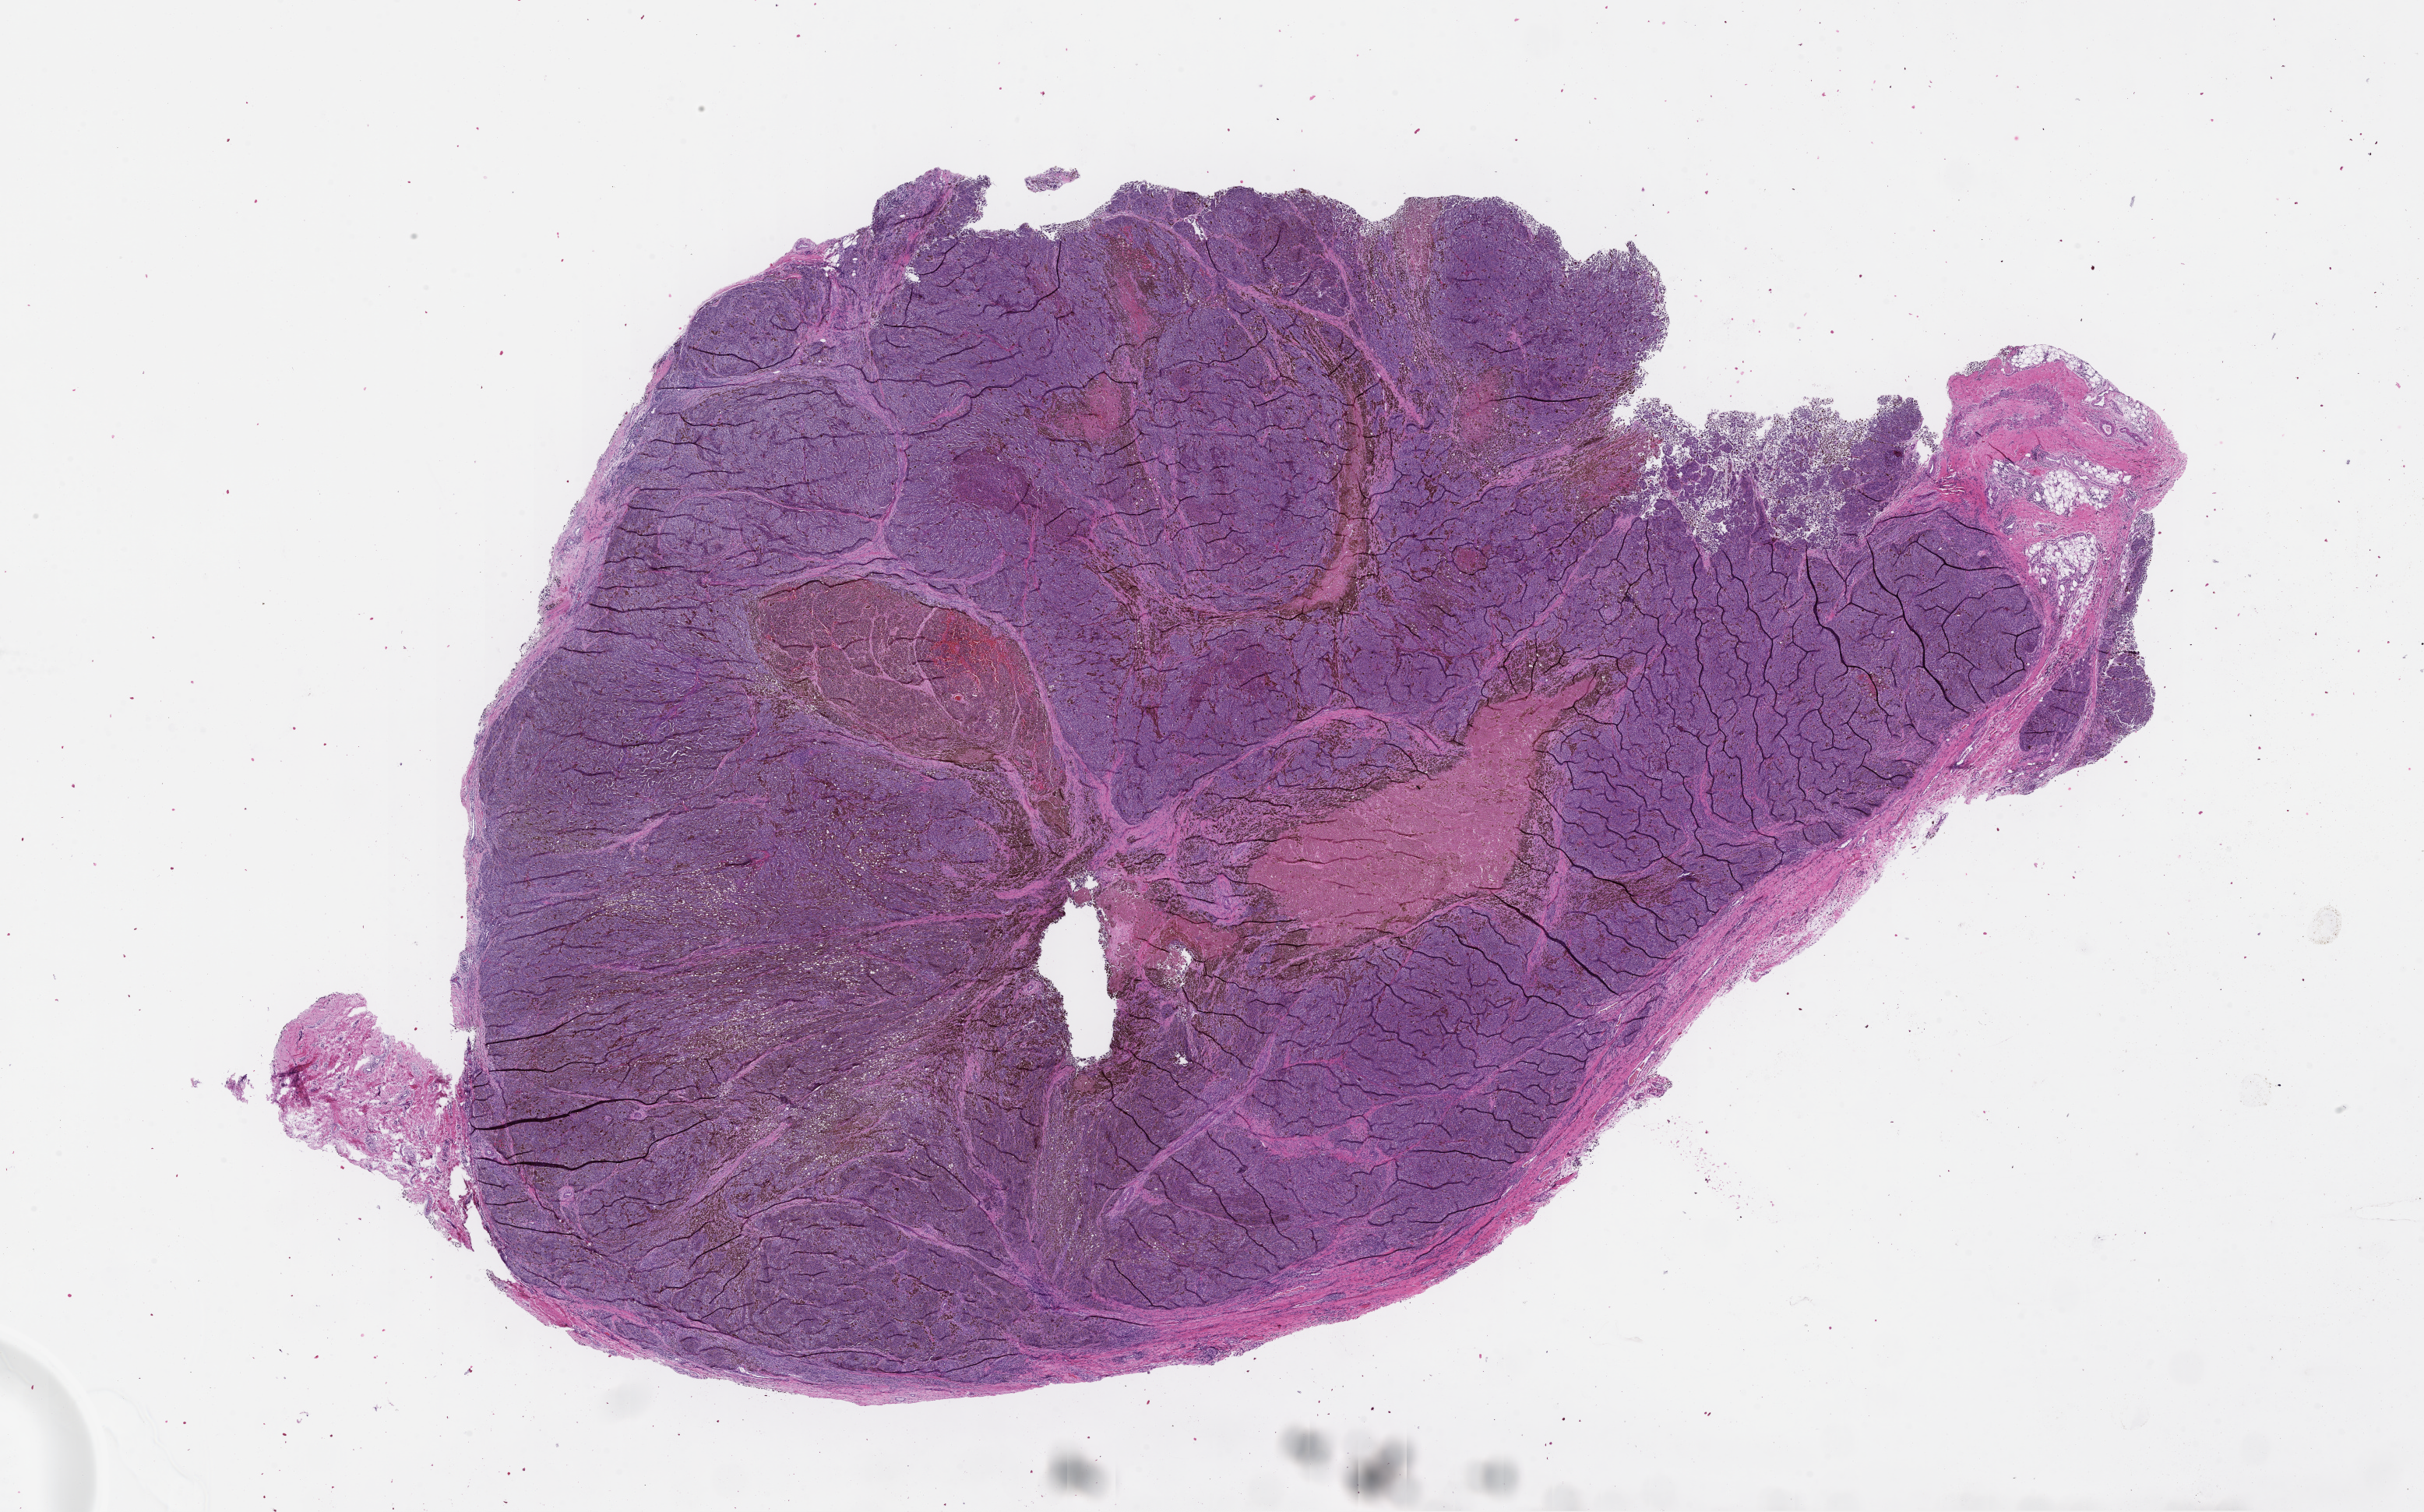
Digitized haematoxylin and eosin-stained section — shown as a low-resolution overview of the whole scanned area (about 25.1 x 15.7 mm). FFPE section. Tissue site: skin. Specimen time point: collected at baseline (before treatment). Patient sex: male.
- patient diagnosis: Melanoma